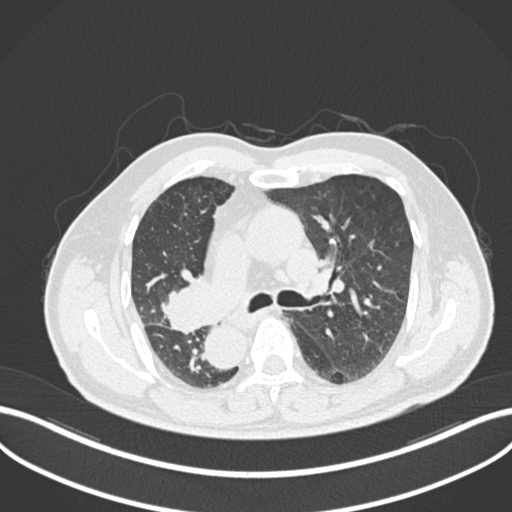
Chest CT, one axial slice. Position 144 of 206 along the scan axis. 120 kVp. Lung window (W 1500 / L -600 HU). 1 mm slice thickness. 512 × 512 image matrix. Patient: male, 67 years. Case-level facts recorded for this patient, not image findings: clinical TNM (as recorded): T2a N0 M0.
Structures marked on this image (rectangle marked by the reading radiologist):
- lung tumour (recorded histology: squamous cell carcinoma): box from (x=159, y=271) to (x=216, y=336) px